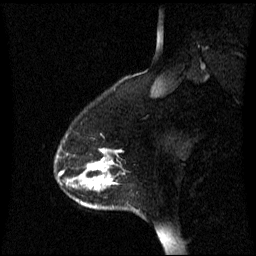
Breast MRI (dynamic contrast-enhanced), one sagittal slice; dynamic contrast-enhanced series, image 2 of 3 at this slice position (ordered by acquisition); 1.5 T; TE 4.2 ms, TR 8.4 ms; 2.2 mm slice thickness; 256 × 256 image matrix, field of view 240 × 240 mm. Patient: female, 45 years. From the clinical record (not read from this slice): setting: breast cancer imaged before/during neoadjuvant chemotherapy; receptor status: HR-positive, HER2-negative.
Structures marked on this image (semi-automatically segmented with operator editing):
- analysis volume of interest (the breast-tissue region the enhancement analysis was run in; not a lesion): box from (x=56, y=146) to (x=125, y=209) px
- tumour enhancement mask (voxels above the 70 % enhancement threshold inside the analysis volume of interest): (x=88, y=160)–(x=115, y=191)